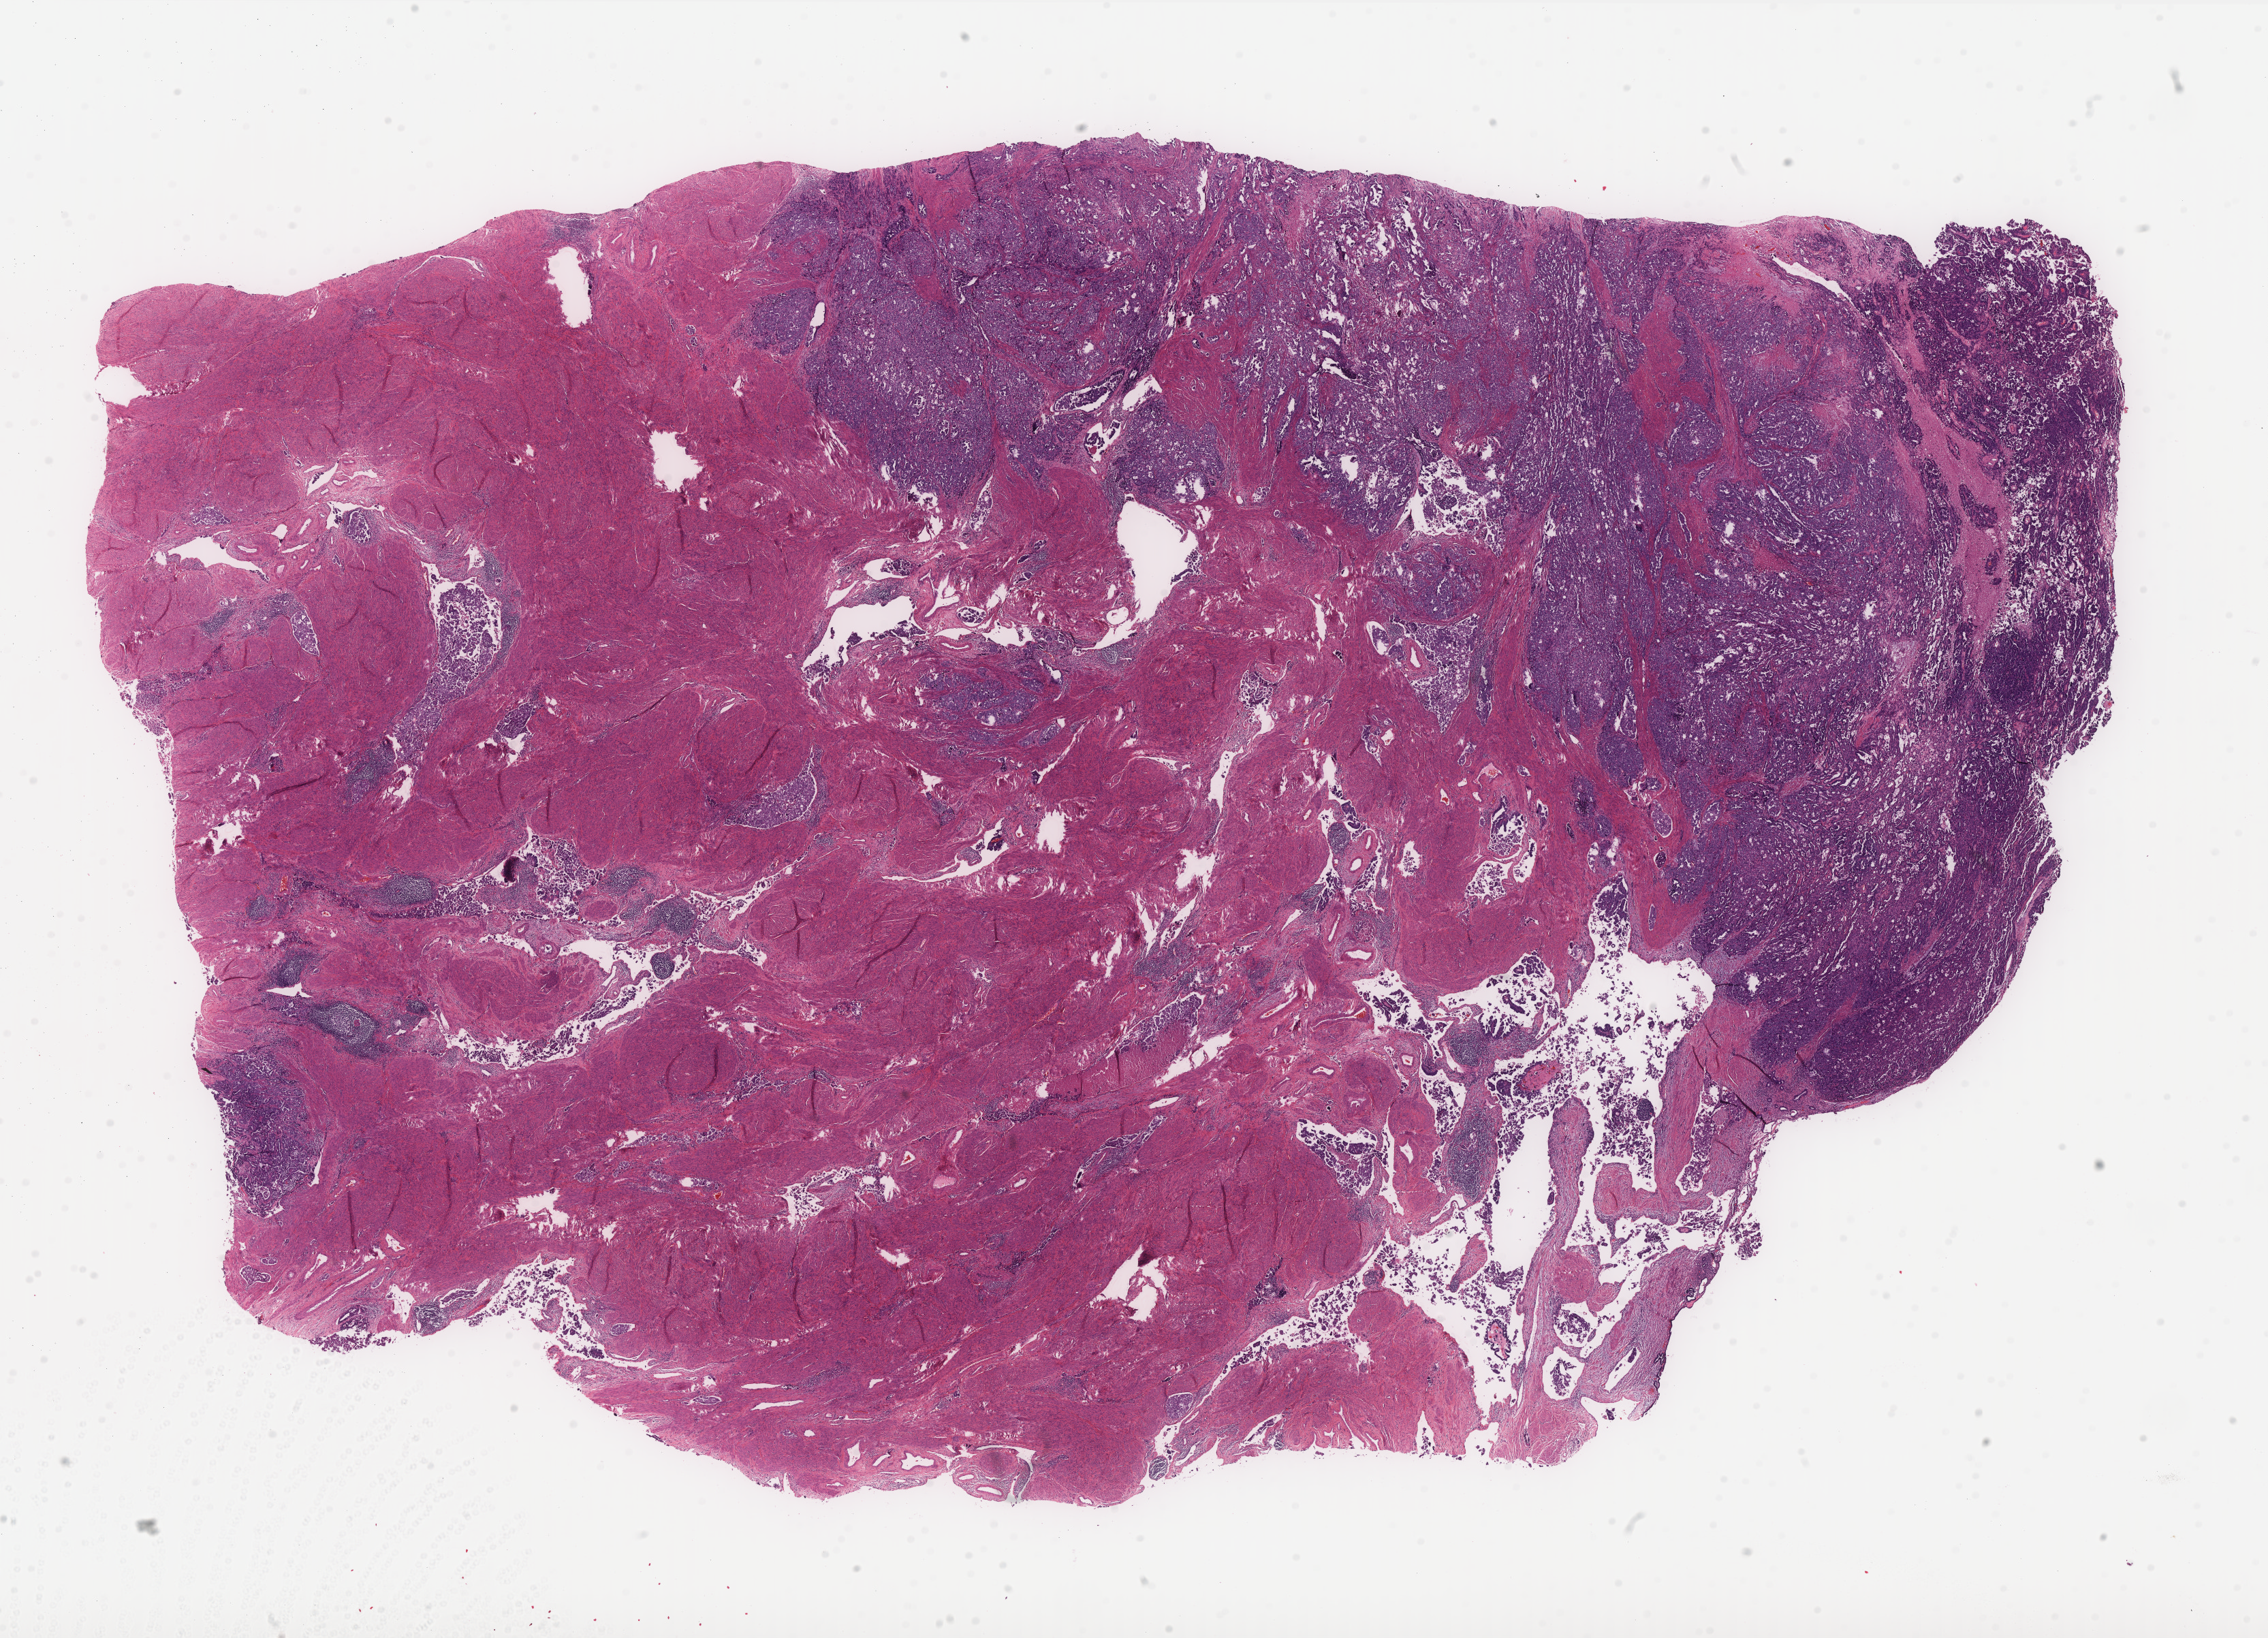
Whole-slide histology image, H&E-stained — whole scanned area (about 26.7 x 19.3 mm, acquisition: 40x scan) shown as a low-resolution overview, formalin-fixed paraffin-embedded (FFPE) diagnostic section, primary tumour sample from the uterus. Patient: female, age at initial diagnosis 61 years. Histologic grade: G3 (poorly differentiated).
• FIGO stage: IIIC2
• diagnosis: Serous cystadenocarcinoma, NOS